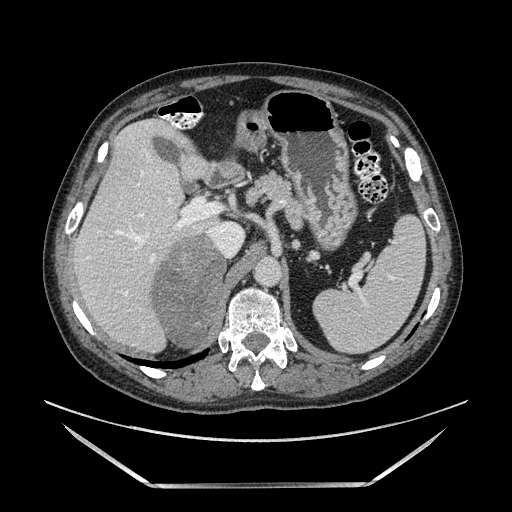
Contrast-enhanced abdominal CT, one axial slice. Slice 96 of 185 in the series (ordered by position). Soft-tissue window (W 400 / L 40 HU). 1.25 mm slice thickness. 512 × 512 image matrix, field of view 440 × 440 mm. Male patient. Case-level facts recorded for this patient, not image findings: diagnosis: adrenocortical carcinoma; tumour side: right adrenal; tumour size at pathology: 10.3 cm; Ki-67 index: 20 %.
Outlined on this slice (semi-automatically segmented with operator editing):
- mass: bounding box <153,231,227,344> (left, top, right, bottom; pixels)